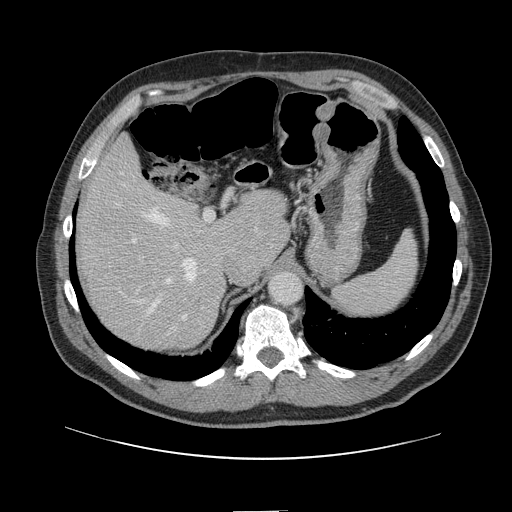
Contrast-enhanced abdominal CT, one axial slice; position 99 of 161 along the scan axis; 120 kVp; intravenous contrast given; soft-tissue window (W 400 / L 40 HU); 2.5 mm slice thickness; 512 × 512 image matrix. Male patient, age 66 years. From the clinical record (not read from this slice): diagnosis: colorectal cancer liver metastases, imaged before liver resection; multiple liver metastases: no; largest metastasis: 3.5 cm.
Annotated regions visible in this slice (outlined manually by an expert reader):
- hepatic veins: bounding box (x1, y1, x2, y2) in pixels: (118, 173, 196, 314)
- liver: (81, 143, 286, 350)
- planned liver remnant (the part of the liver to remain after resection): (81, 142, 286, 306)
- portal vein (with intrahepatic branches): (129, 211, 216, 309)